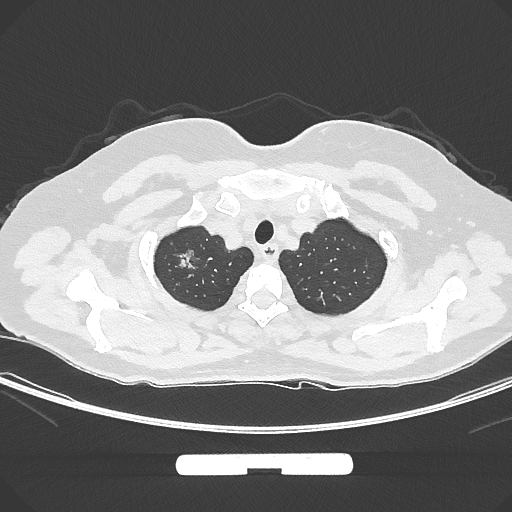
Chest CT, one axial slice. Position 261 of 294 along the scan axis. Reconstruction kernel IMR1,SharpPlus. Lung window (W 1500 / L -600 HU). 1 mm slice thickness. 512 × 512 image matrix, field of view 369 × 369 mm. Female patient, age 58 years. From the clinical record (not read from this slice): clinical TNM (as recorded): T1b N0 M0; histopathological grade: G2-3.
Annotated regions visible in this slice (bounding box drawn by a radiologist):
- lung tumour (recorded histology: adenocarcinoma): bounding box [x1, y1, x2, y2] px = [172, 242, 200, 278]